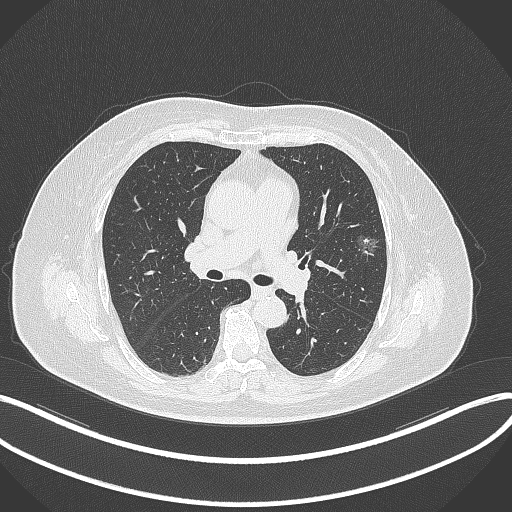
Chest CT, one axial slice; position 212 of 315 along the scan axis; reconstruction kernel B70f; 120 kVp; lung window (W 1500 / L -600 HU); 1 mm slice thickness; 512 × 512 image matrix. Patient: female, 76 years. Case-level facts recorded for this patient, not image findings: clinical TNM (as recorded): T1b N0 M0; histopathological grade: G1-2.
Outlined on this slice (rectangle marked by the reading radiologist):
- lung tumour (recorded histology: adenocarcinoma): bounding box <355,228,383,262> (left, top, right, bottom; pixels)